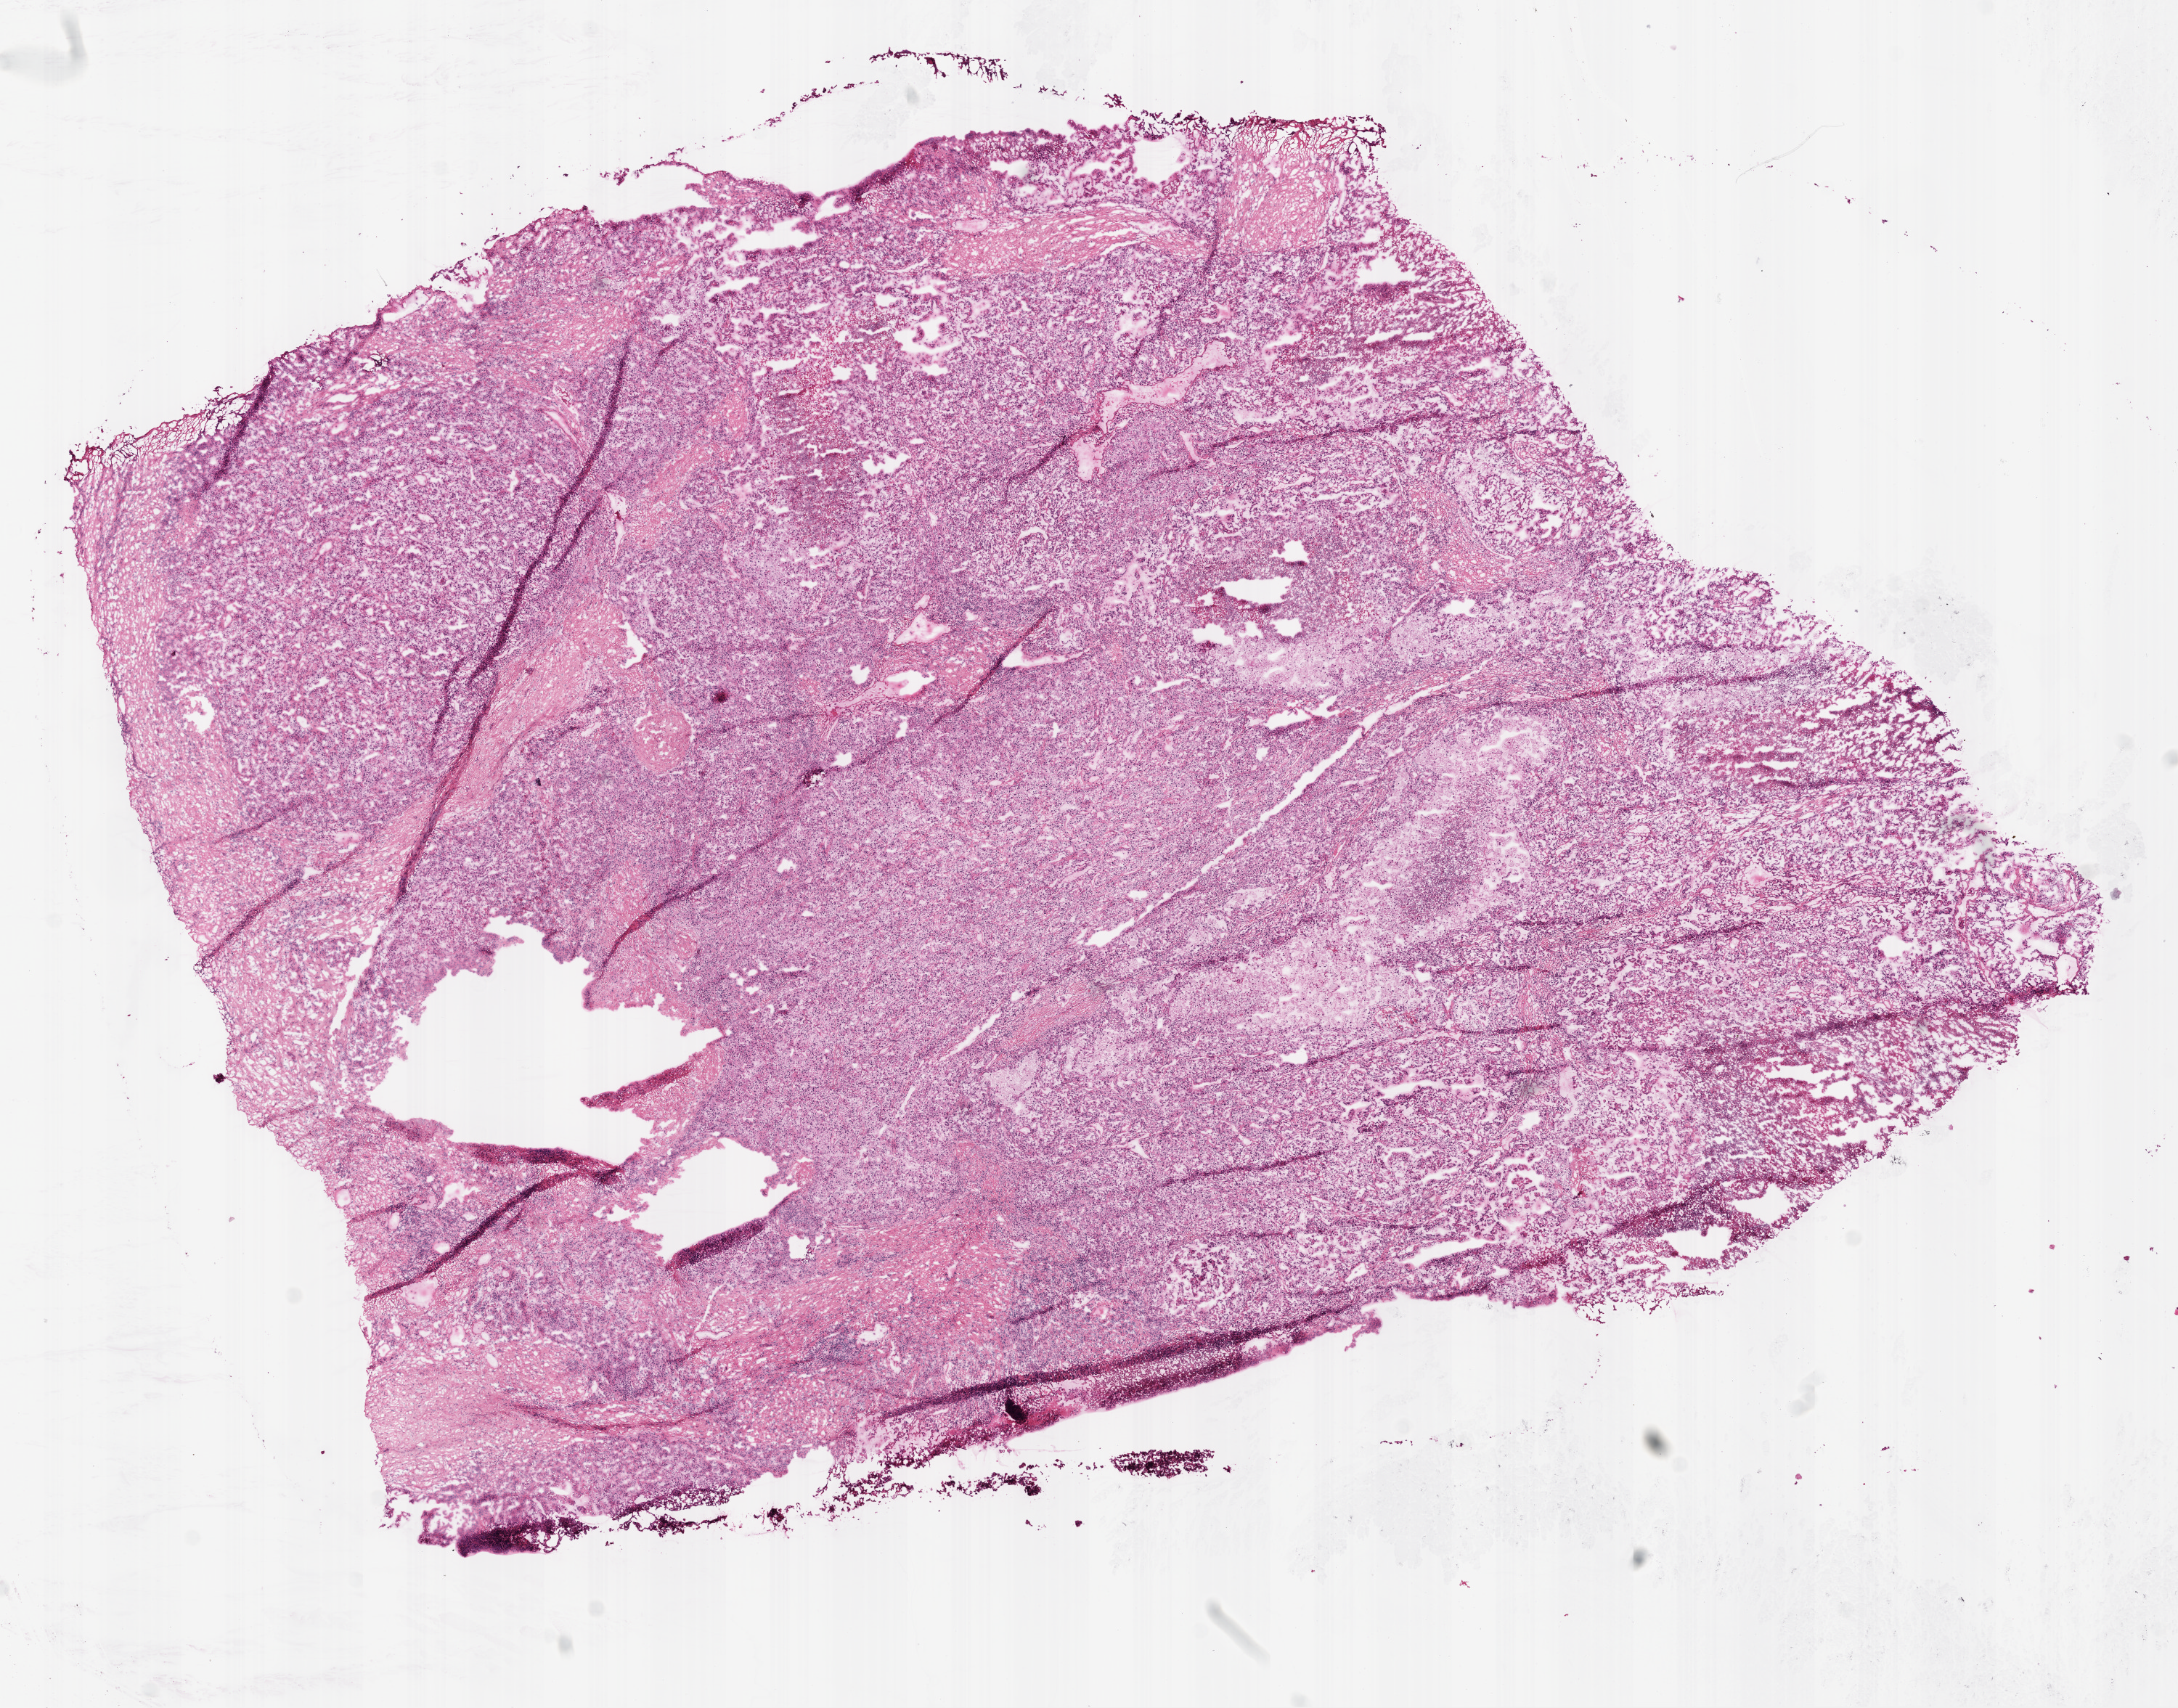
Digitized H&E-stained tissue section (whole slide), low-resolution overview of the scanned area, about 12.0 x 9.4 mm (slide scanned at 20x). Frozen section from the top of the tissue portion. Primary tumour sample from the kidney. Male patient; age at initial diagnosis 37 years. Histologic grade: G3 (poorly differentiated). Pathologist review of this section (percent, as recorded): tumour cells 82%, tumour nuclei 75%, normal cells 0%, stromal cells 10%, necrosis 8%.
Lymph nodes positive (case pathology): 3 of 10 examined. Histologic diagnosis: Clear cell adenocarcinoma, NOS. TNM: T3a N1 M0. Laterality: right. AJCC pathologic stage: III (7th edition).